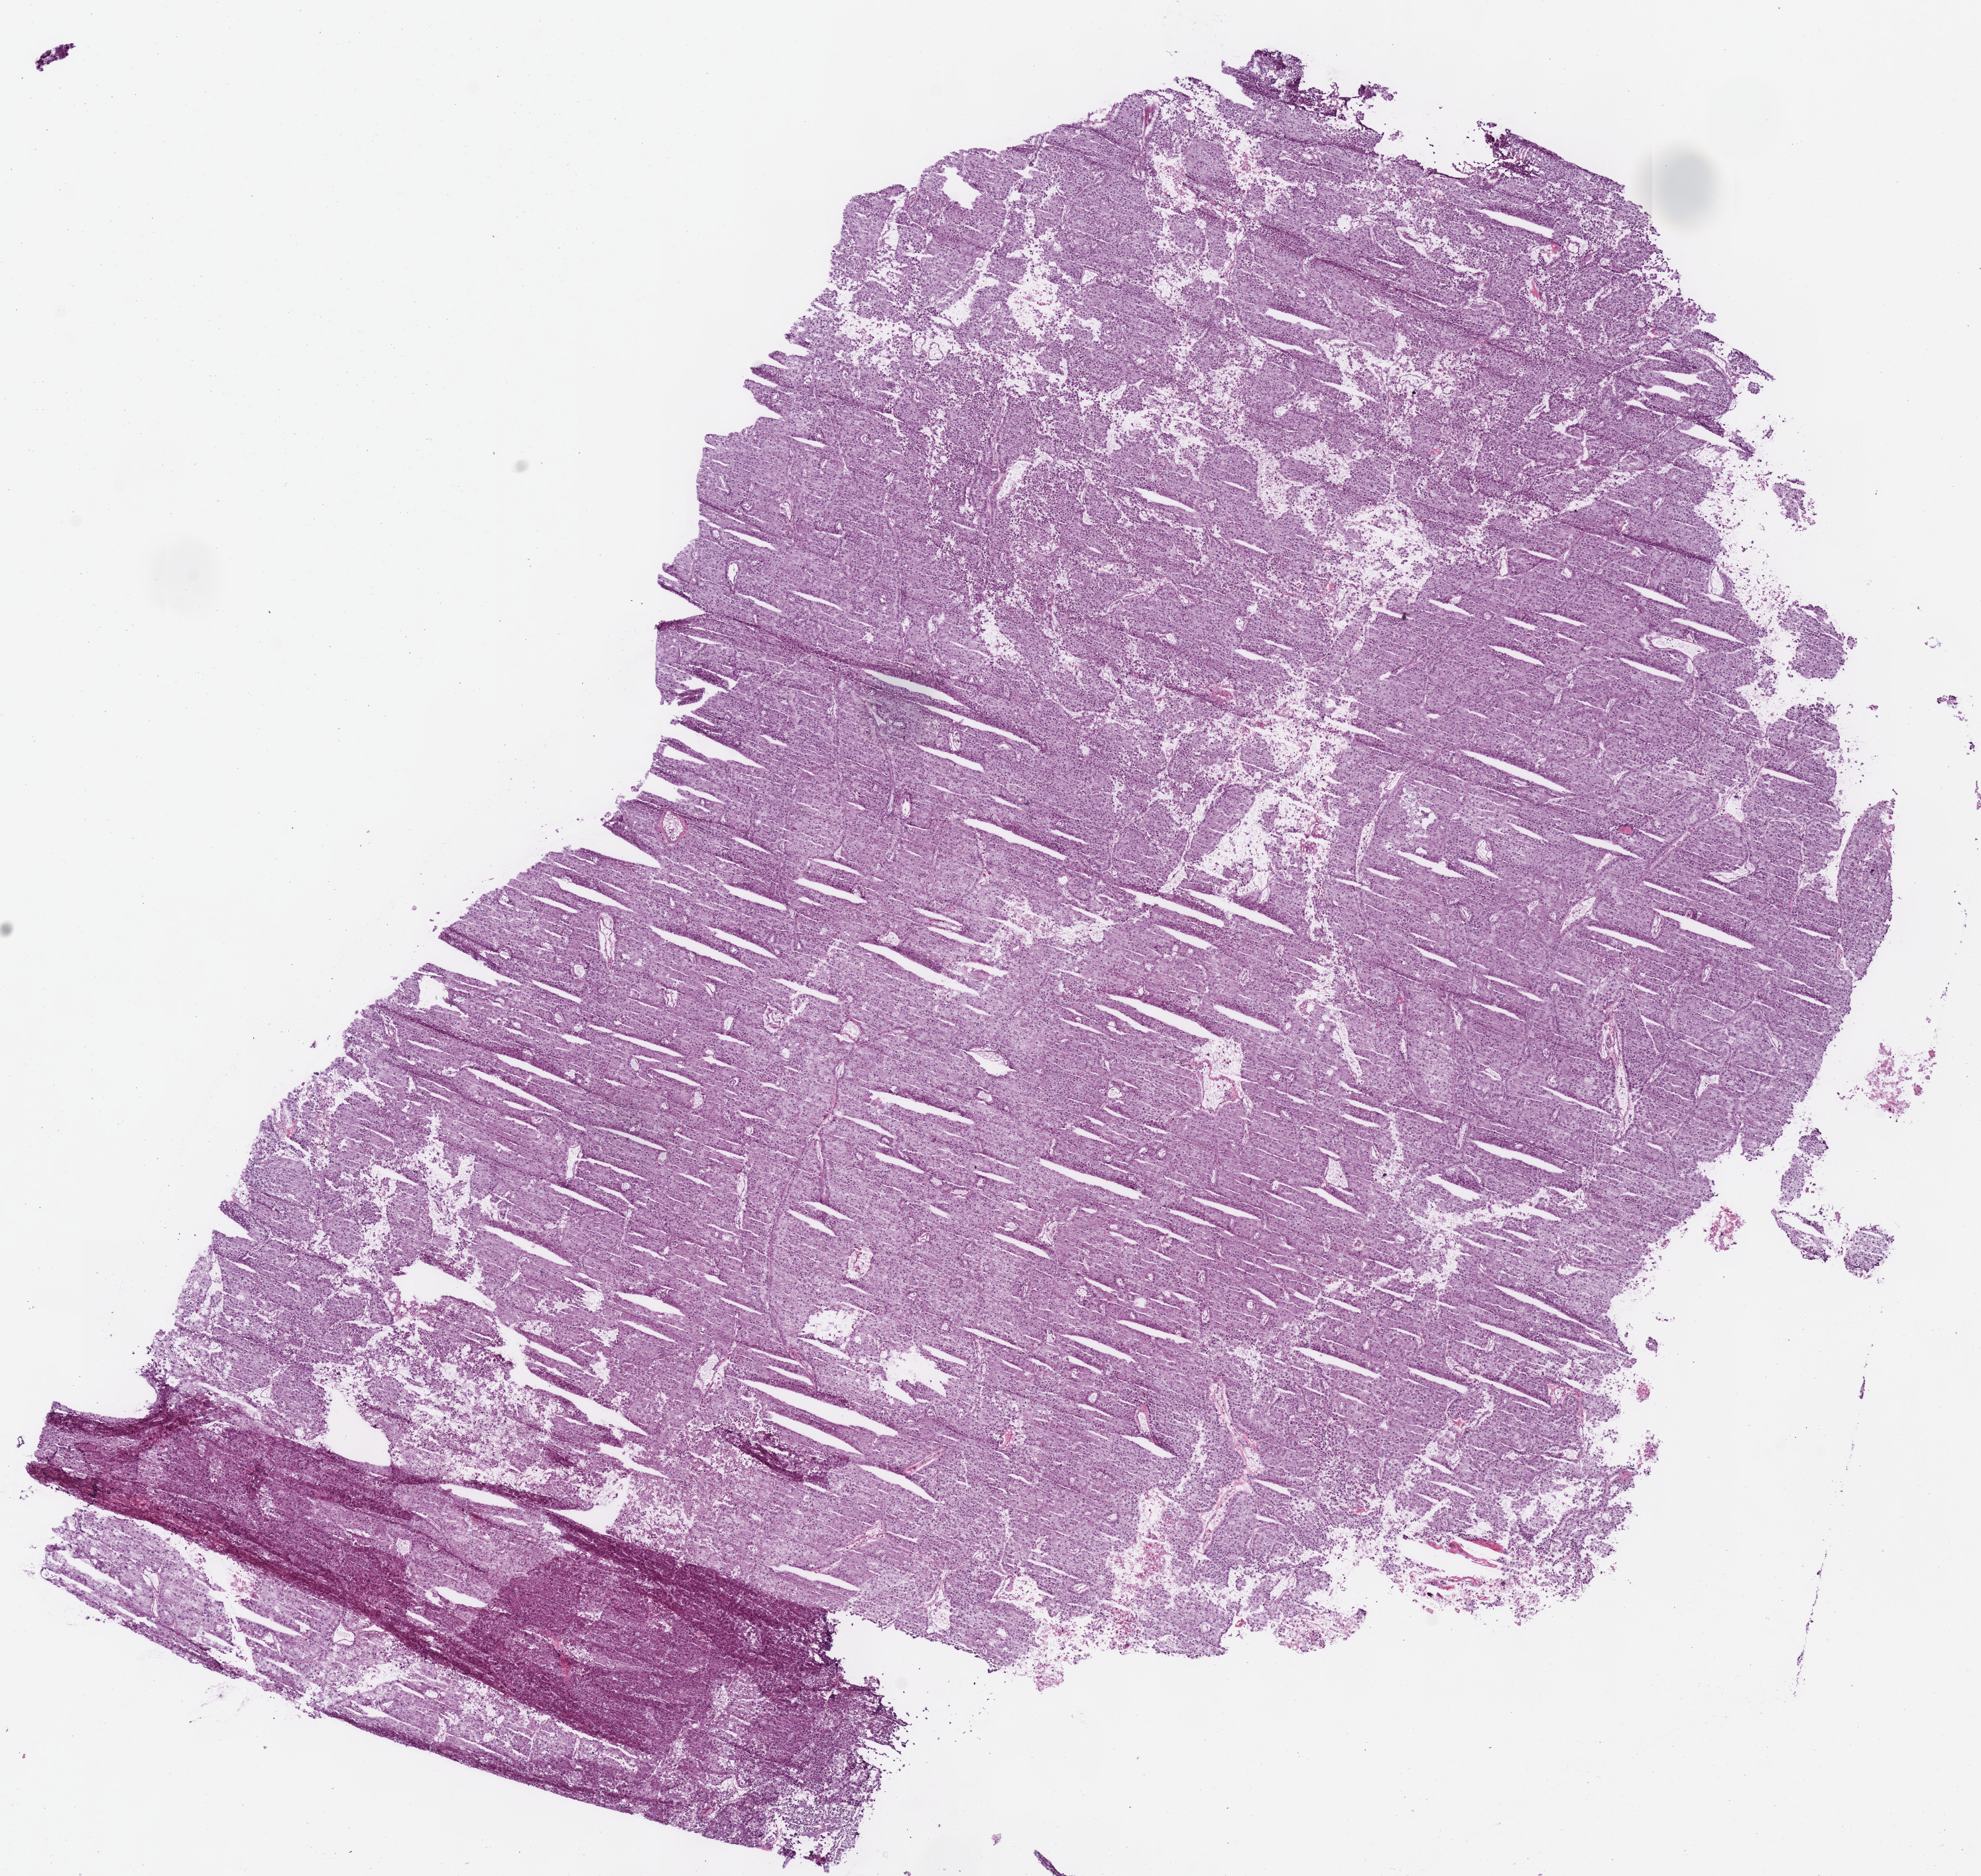
H&E whole-slide image, a low-resolution overview of the entire scanned area, about 11.7 x 11.1 mm. Frozen section. Primary tumour sample from the kidney. Male, age 41 years at initial diagnosis. Pathologist review of this section (percent, as recorded): tumour cells 90%, tumour nuclei 95%, normal cells 0%, stromal cells 5%, necrosis 5%.
TNM: T3b N2 M0. Laterality: left. Pathologic diagnosis: Renal cell carcinoma, chromophobe type. AJCC pathologic stage: IV (6th edition).